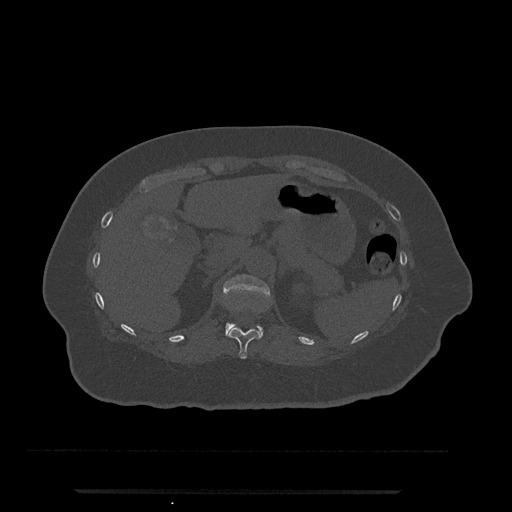
CT including the spine, one axial slice; reconstruction kernel Br40s/3; bone window (W 1800 / L 400 HU); 0.5 mm slice thickness; 512 × 512 image matrix, field of view 440 × 440 mm. Female patient, age 51 years. From the clinical record (not read from this slice): primary cancer: neuro; vertebrae with lytic lesions (as recorded): T8.
Outlined on this slice (semi-automatically segmented with operator editing):
- T11 vertebra: box from (x=226, y=327) to (x=261, y=359) px
- T12 vertebra: (x=223, y=274)–(x=270, y=337)